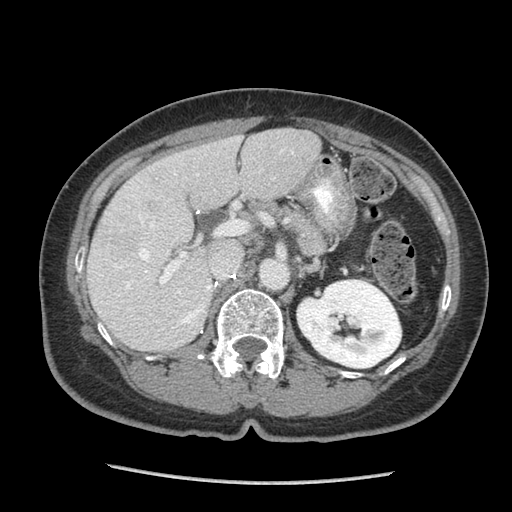
Contrast-enhanced abdominal CT (liver protocol), one axial slice. Position 44 of 105 along the scan axis. Reconstruction kernel STANDARD. 140 kVp. Soft-tissue window (W 400 / L 40 HU). 2.5 mm slice thickness. 512 × 512 image matrix. Case-level facts recorded for this patient, not image findings: diagnosis: hepatocellular carcinoma (patient treated with transarterial chemoembolisation; whether this scan precedes or follows treatment is not stated here); TNM stage (as recorded): Stage-I; Child-Pugh class: A; tumour differentiation: moderately differentiated.
Outlined on this slice (semi-automatically segmented with operator editing):
- liver parenchyma outside the tumour (the mass and vessels are separate outlines, so this box may not span the whole liver): bounding box [x1, y1, x2, y2] px = [86, 128, 320, 350]
- liver vessels: [101, 138, 294, 324]